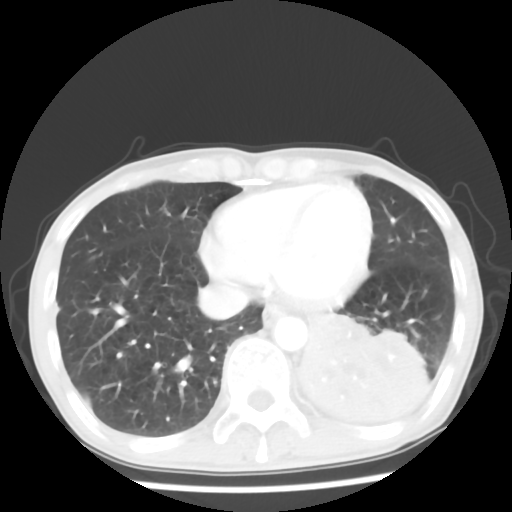
Chest CT, one axial slice; reconstruction kernel STANDARD; 120 kVp; lung window (W 1500 / L -600 HU); 5 mm slice thickness; 512 × 512 image matrix. Patient: male, 68 years. Case-level facts recorded for this patient, not image findings: clinical TNM (as recorded): T4 N0 M0.
Outlined on this slice (rectangle marked by the reading radiologist):
- lung tumour (recorded histology: squamous cell carcinoma): box from (x=284, y=313) to (x=448, y=453) px